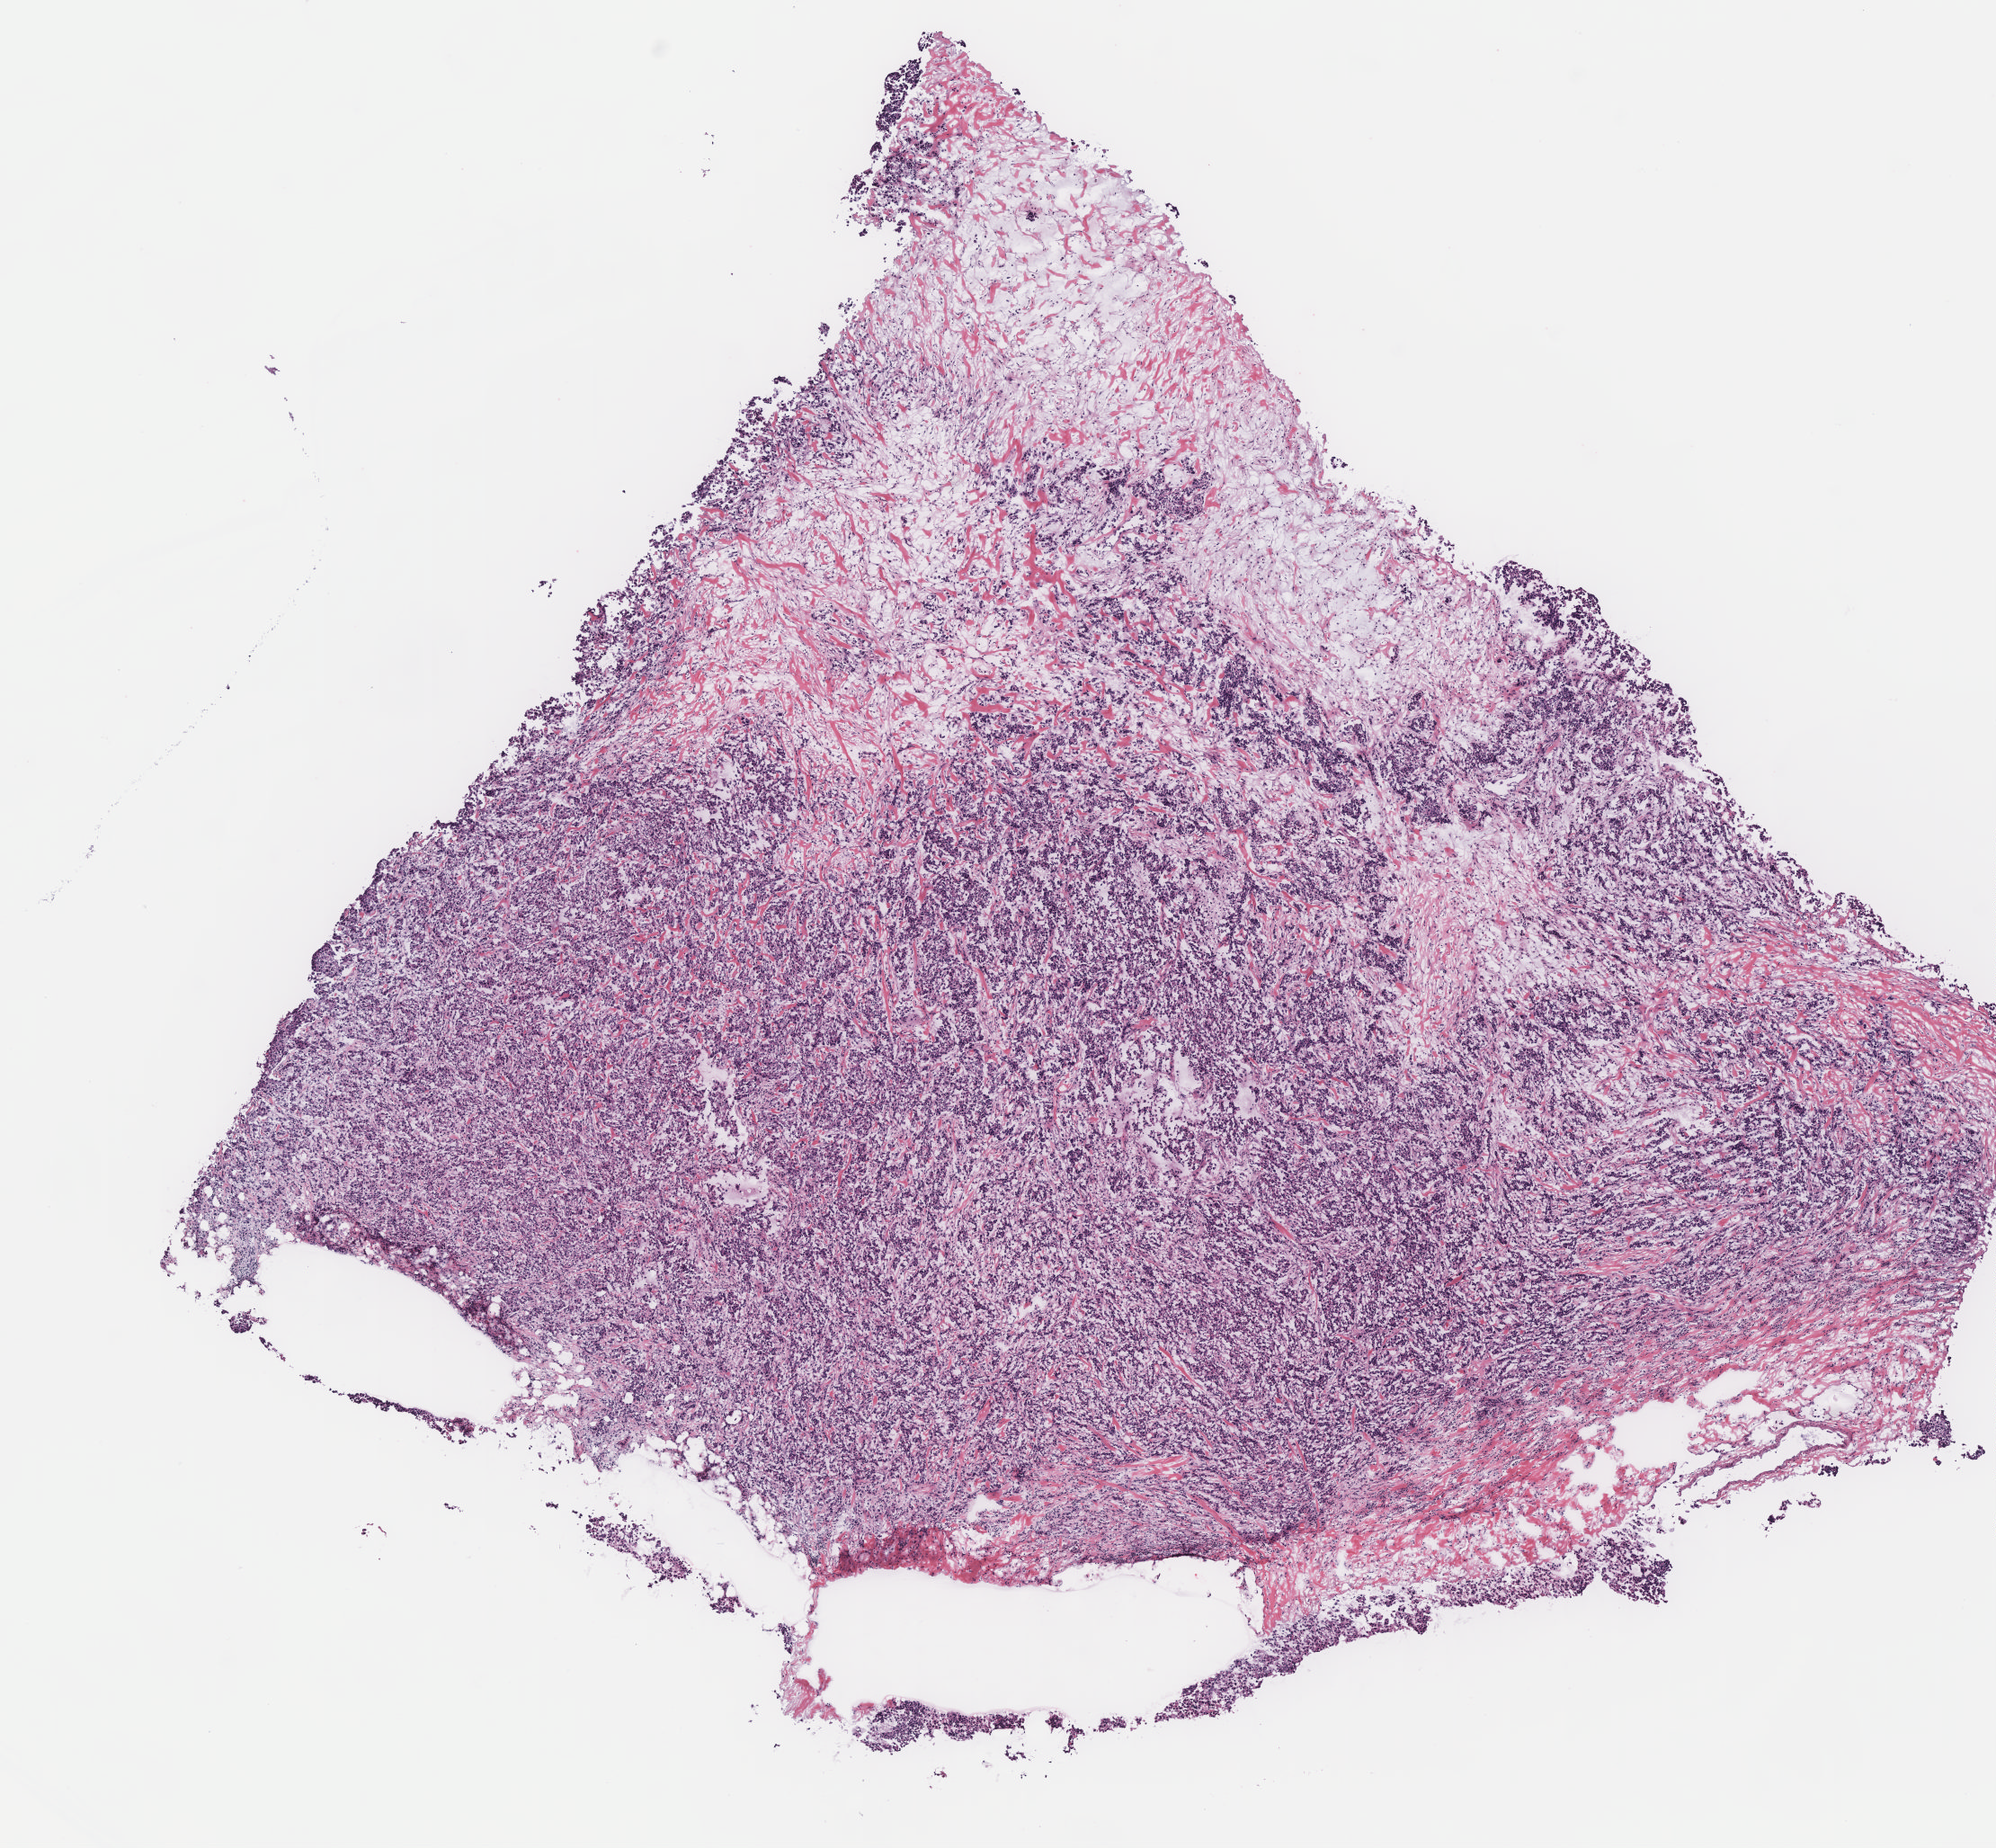
Hematoxylin and eosin (H&E) stained whole-slide image, shown as a low-resolution overview of the whole scanned area (about 8.9 x 8.2 mm); breast, tissue type not recorded. Patient: female, age 74 years.
Patient diagnosis: Infiltrating duct carcinoma, NOS.